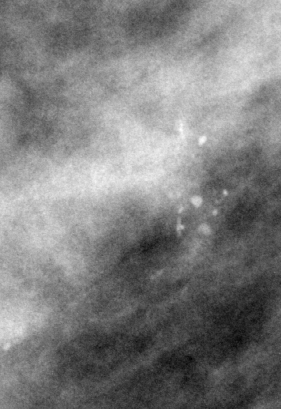
Region of interest cut from a scanned film mammogram (one marked finding); right breast; CC view.
Finding: calcifications, morphology pleomorphic, distribution clustered; BI-RADS assessment category 5; subtlety rating 4 on a 1 (subtle) to 5 (obvious) scale; pathology (as recorded): malignant.